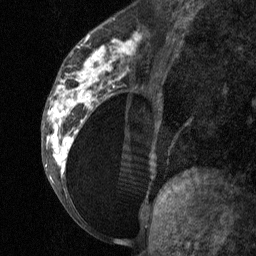
Breast MRI (dynamic contrast-enhanced), one sagittal slice. Dynamic contrast-enhanced study with each time point stored as its own series, time point 2 of 3 at this slice position (early post-contrast, ordered by acquisition time). 1.5 T. TE 4.8 ms, TR 27 ms. 2 mm slice thickness. 256 × 256 image matrix, field of view 180 × 180 mm. Female patient, age 34 years. From the clinical record (not read from this slice): setting: breast cancer imaged before/during neoadjuvant chemotherapy; receptor status: HR-positive, HER2-negative.
Annotated regions visible in this slice (semi-automatic segmentation, software-assisted and operator-edited):
- analysis volume of interest (the breast-tissue region the enhancement analysis was run in; not a lesion): bounding box [x1, y1, x2, y2] px = [41, 23, 157, 197]
- tumour enhancement mask (voxels above the 90 % enhancement threshold inside the analysis volume of interest): [47, 33, 141, 177]